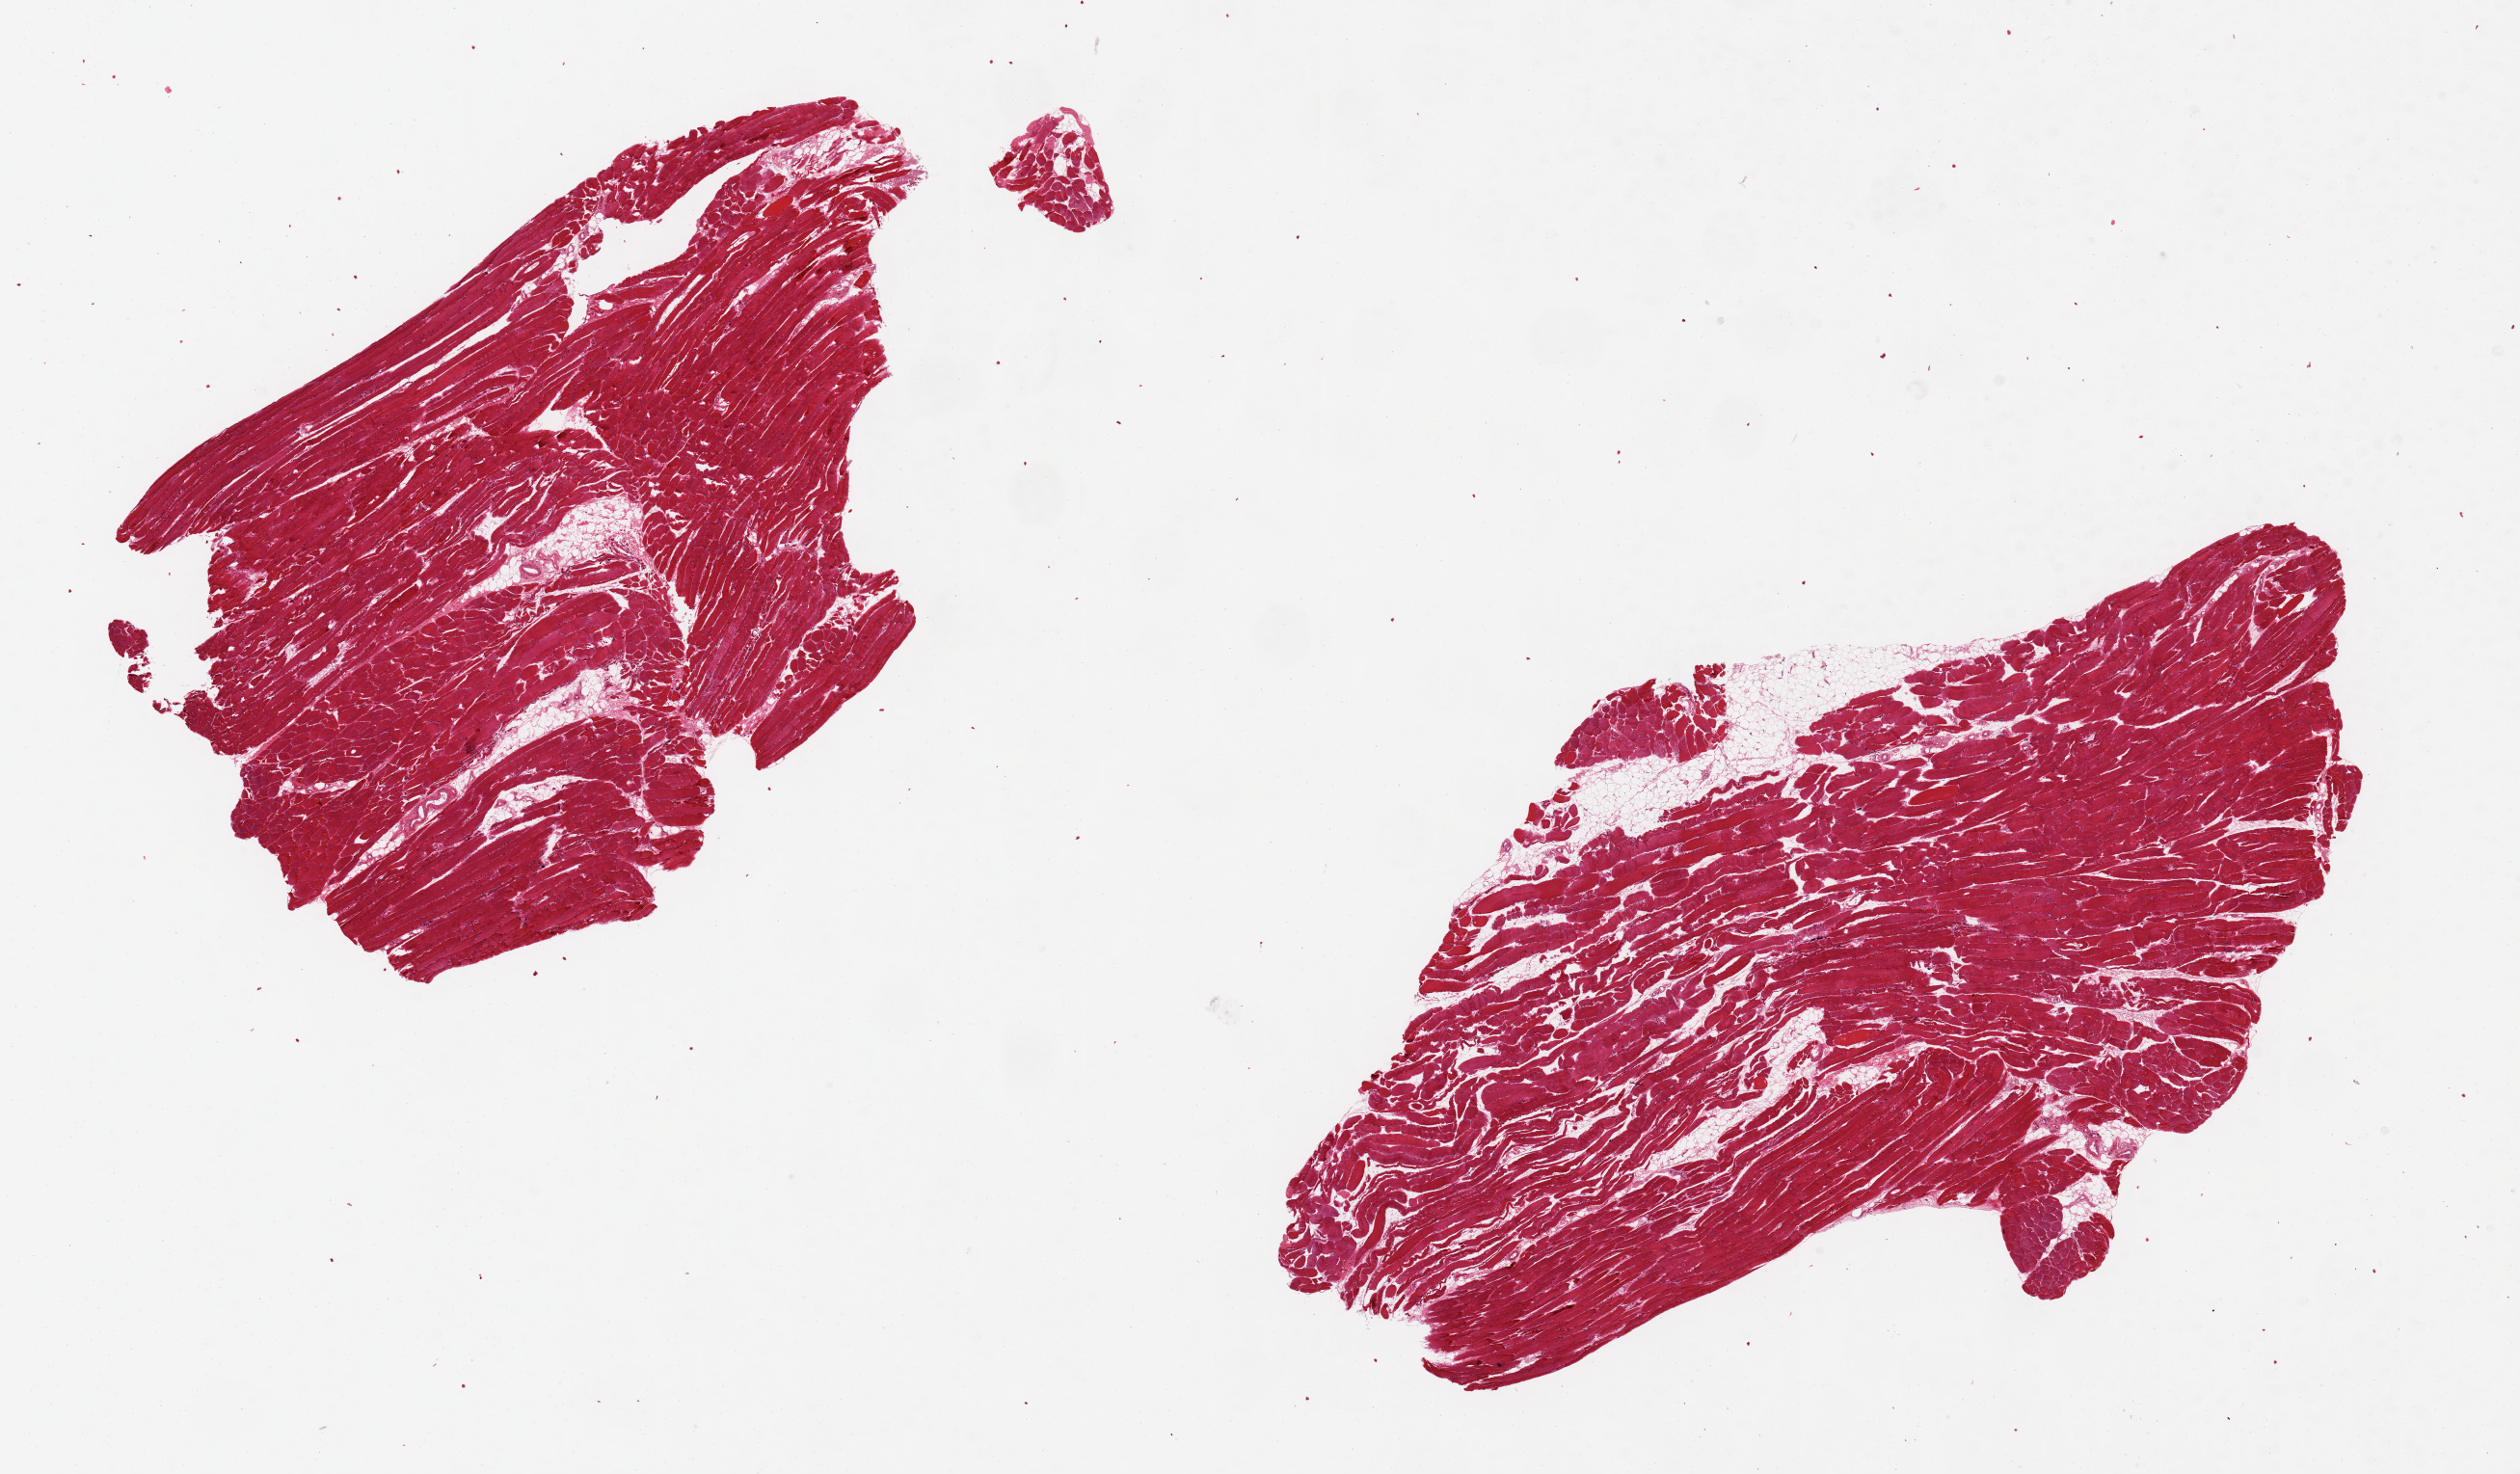
Hematoxylin and eosin (H&E) whole-slide image — whole scanned area (about 20.7 x 12.1 mm, acquisition: 20x scan) shown as a low-resolution overview; PAXgene-fixed, paraffin-embedded tissue; sampled site (target tissue): skeletal muscle; tissue donor sample. Donor sex: female.
Review note (as recorded): 2 pieces 9x4 & 7x5 mm; <10% internal adipose.